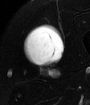
MRI of an extremity soft-tissue mass, one axial slice; slice 42 of 65 in the series (ordered by position); T2-weighted fat-saturated; MR volume resampled by the dataset authors to the PET/CT grid (not the native acquisition matrix); 3.27 mm slice thickness; 90 × 105 image matrix. Male patient. From the clinical record (not read from this slice): histological type: mixoid liposarcoma; grade: low; site of the primary tumour: left thigh.
Structures marked on this image (expert contour drawn on MRI and transferred to this co-registered scan by the dataset authors):
- gross tumour volume (mass): bounding box <23,27,63,67> (left, top, right, bottom; pixels)